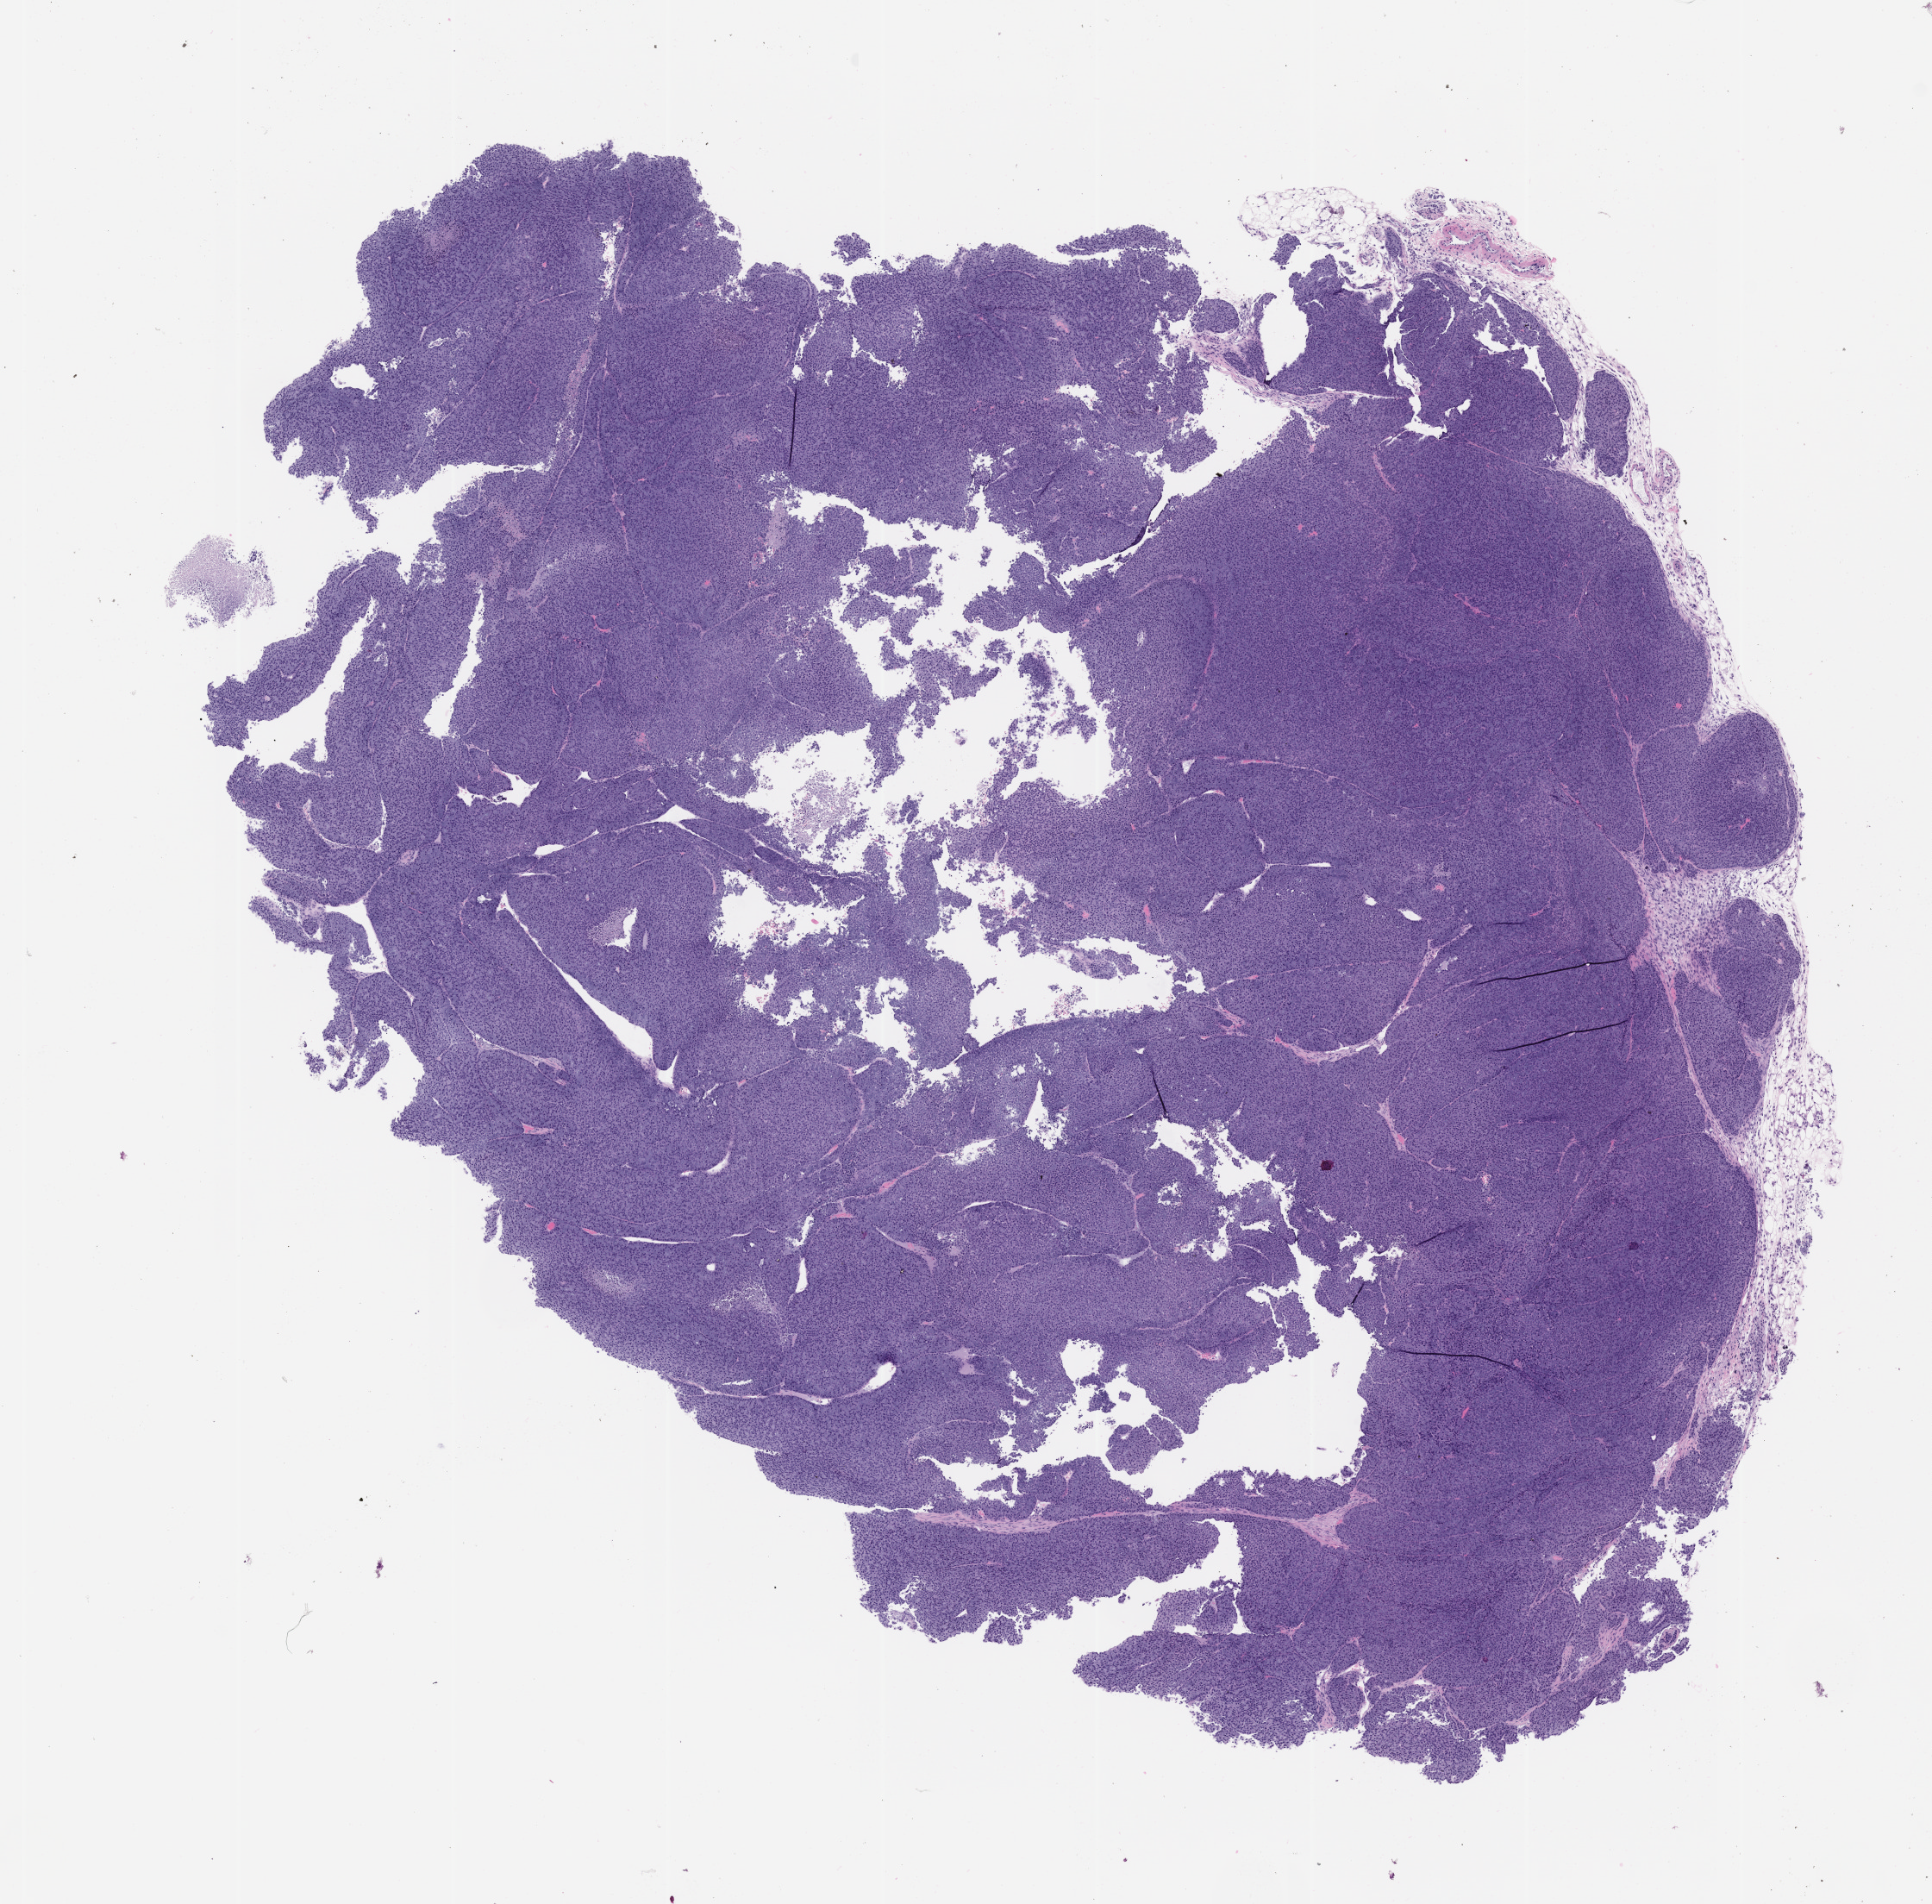
H&E whole-slide image of a patient-derived xenograft (PDX) tumor grown in a mouse, passage 2, shown as a low-resolution overview of the whole scanned area (about 9.0 x 8.9 mm), FFPE section, originating tumor site category: head and neck.
- originating patient diagnosis: Acinar Cell Carcinoma